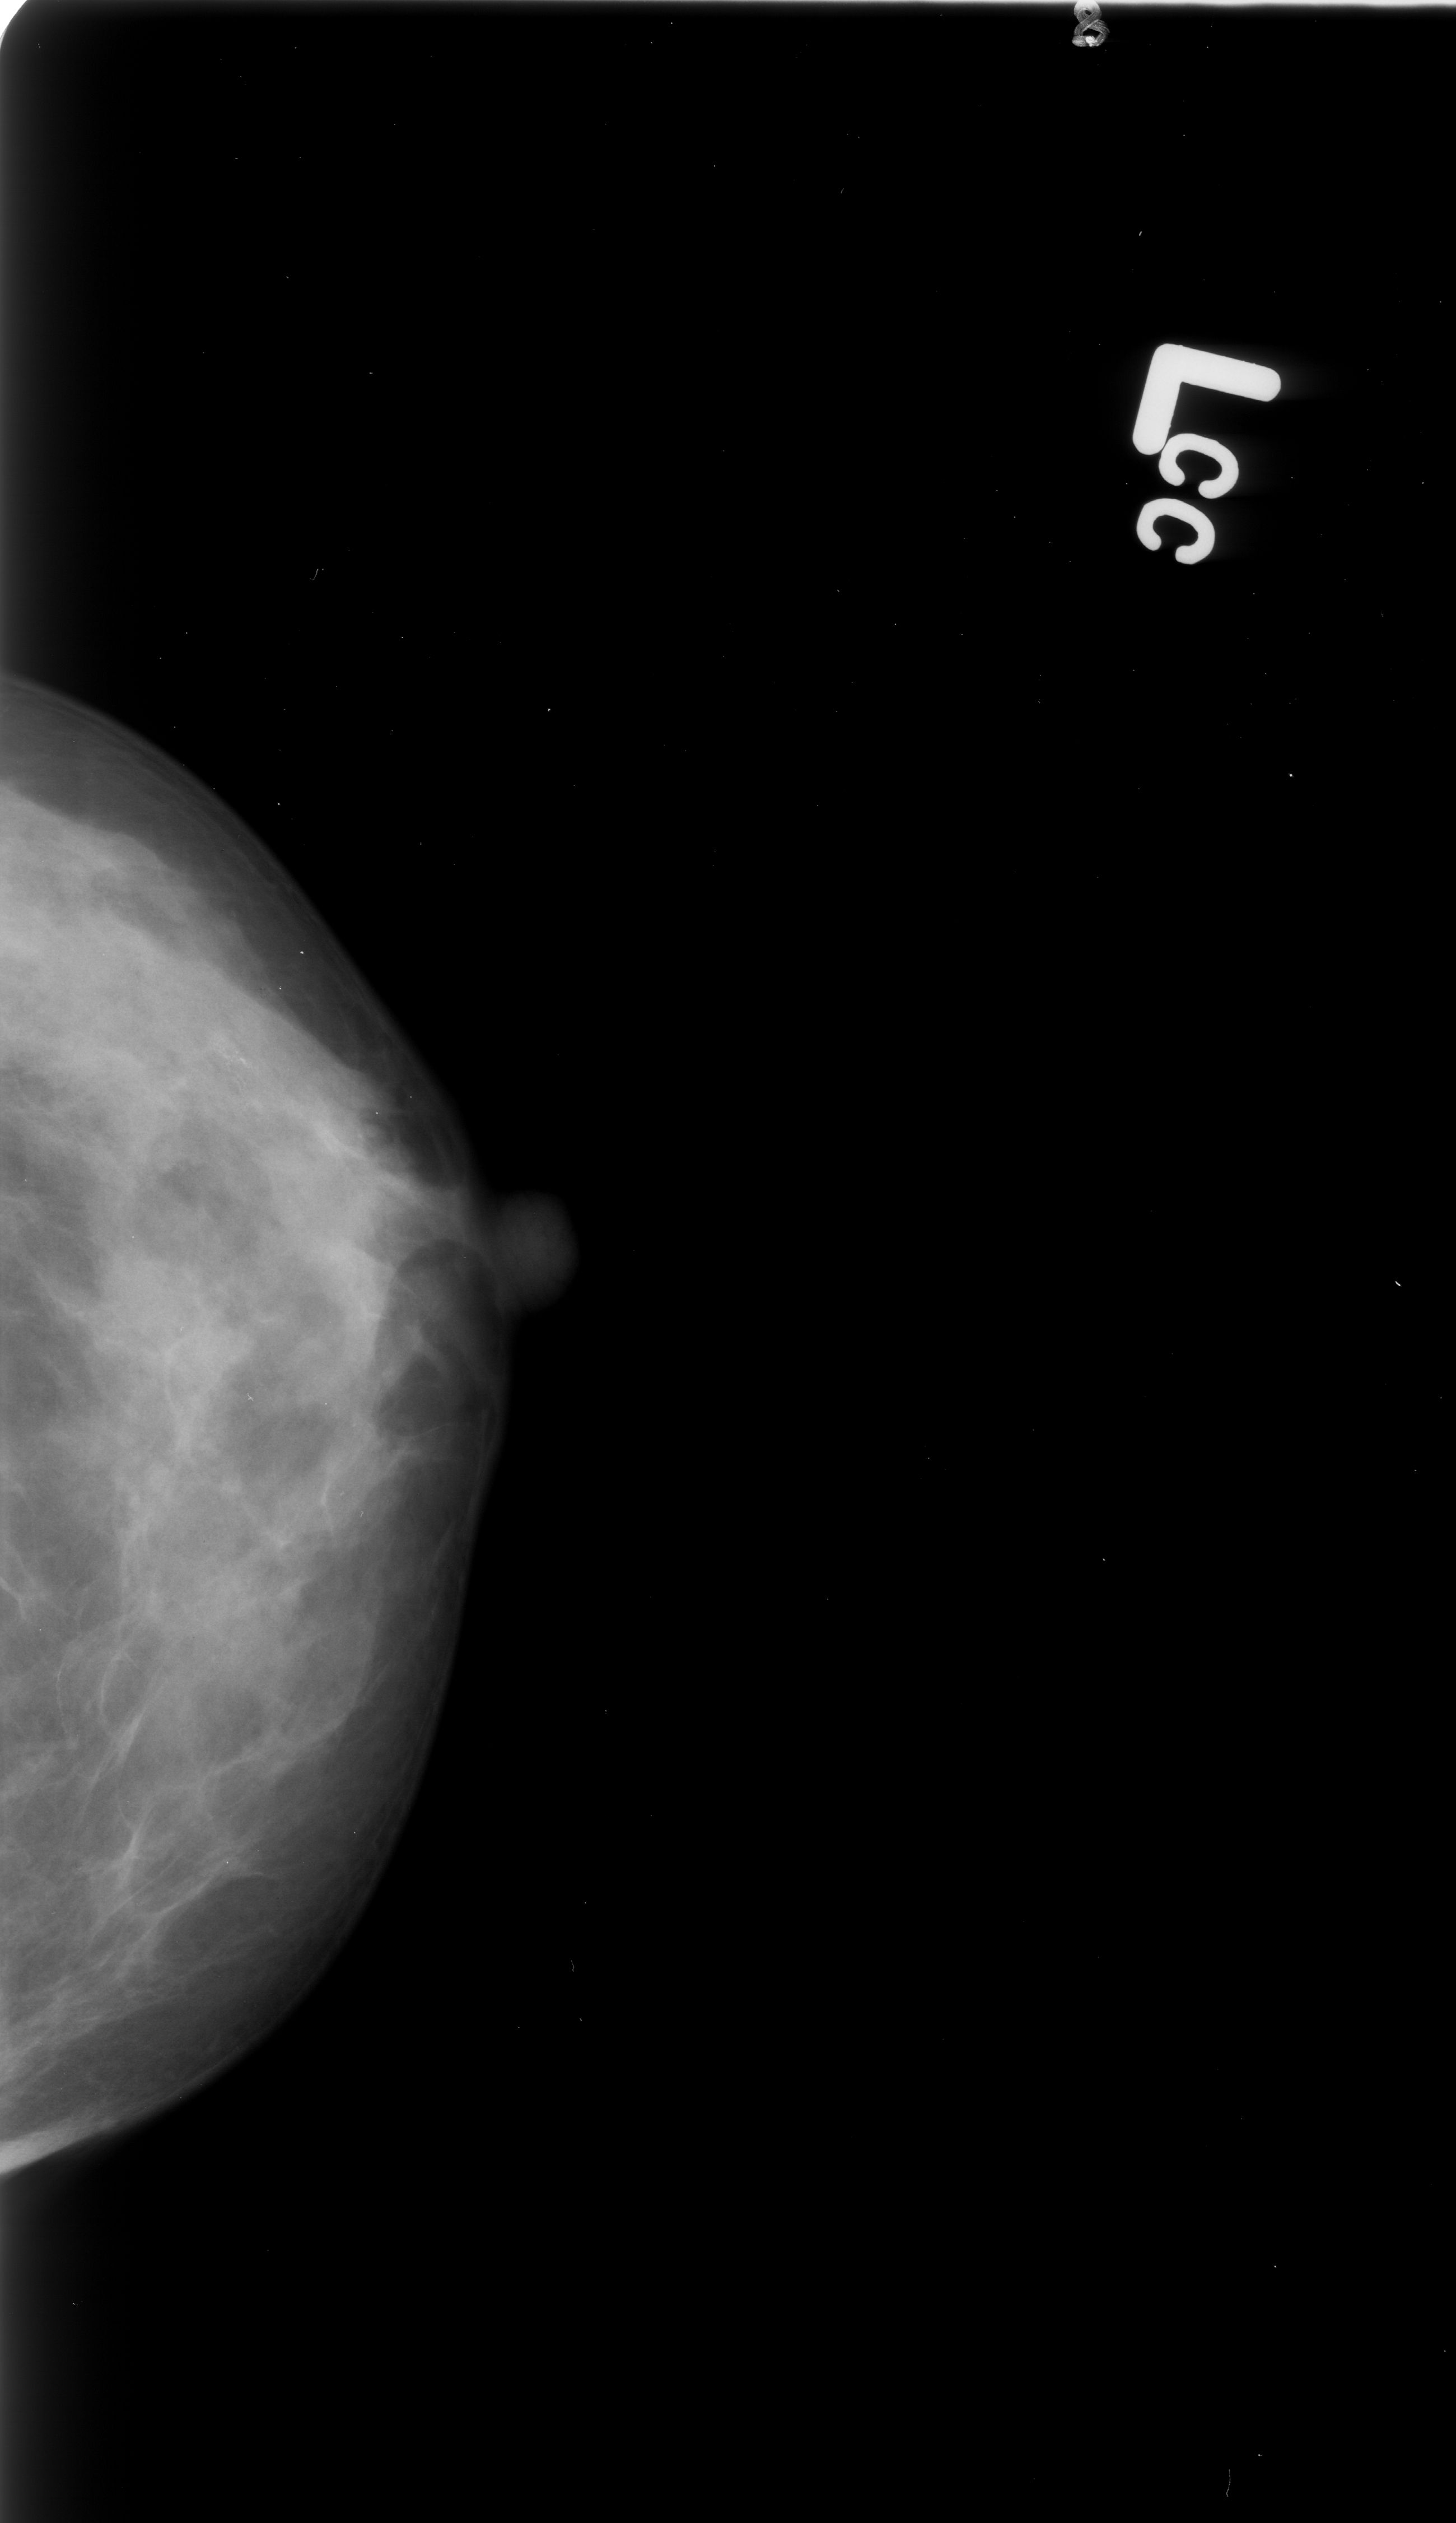
Mammogram (digitized film); left breast; craniocaudal (CC) view; BI-RADS breast density category 3 (scale 1–4); 1456 × 2523 image matrix.
Expert-marked regions of interest on this image (one box per marked abnormality):
- calcifications, morphology punctate / amorphous, distribution clustered / linear; BI-RADS assessment category 4; pathology (as recorded): benign: bounding box [x1, y1, x2, y2] px = [161, 1313, 274, 1395]